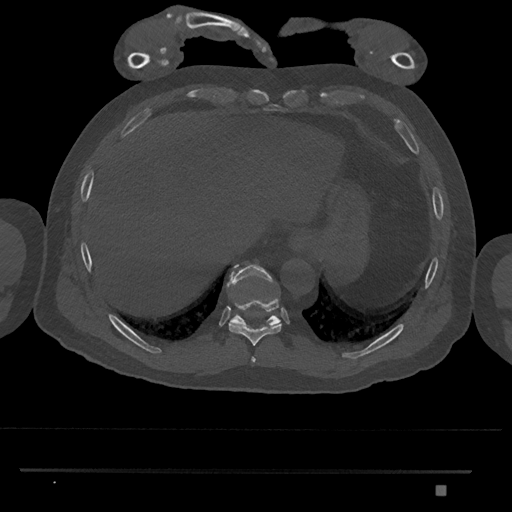
CT including the spine, one axial slice. Position 1038 of 1134 along the scan axis. 120 kVp. Bone window (W 1800 / L 400 HU). 512 × 512 image matrix, field of view 429 × 429 mm. Patient: male, 65 years. From the clinical record (not read from this slice): primary cancer: prostate.
Structures marked on this image (semi-automatically segmented with operator editing):
- T10 vertebra: box from (x=227, y=264) to (x=281, y=327) px
- T8 vertebra: (x=251, y=357)–(x=256, y=363)
- T9 vertebra: (x=228, y=299)–(x=282, y=346)